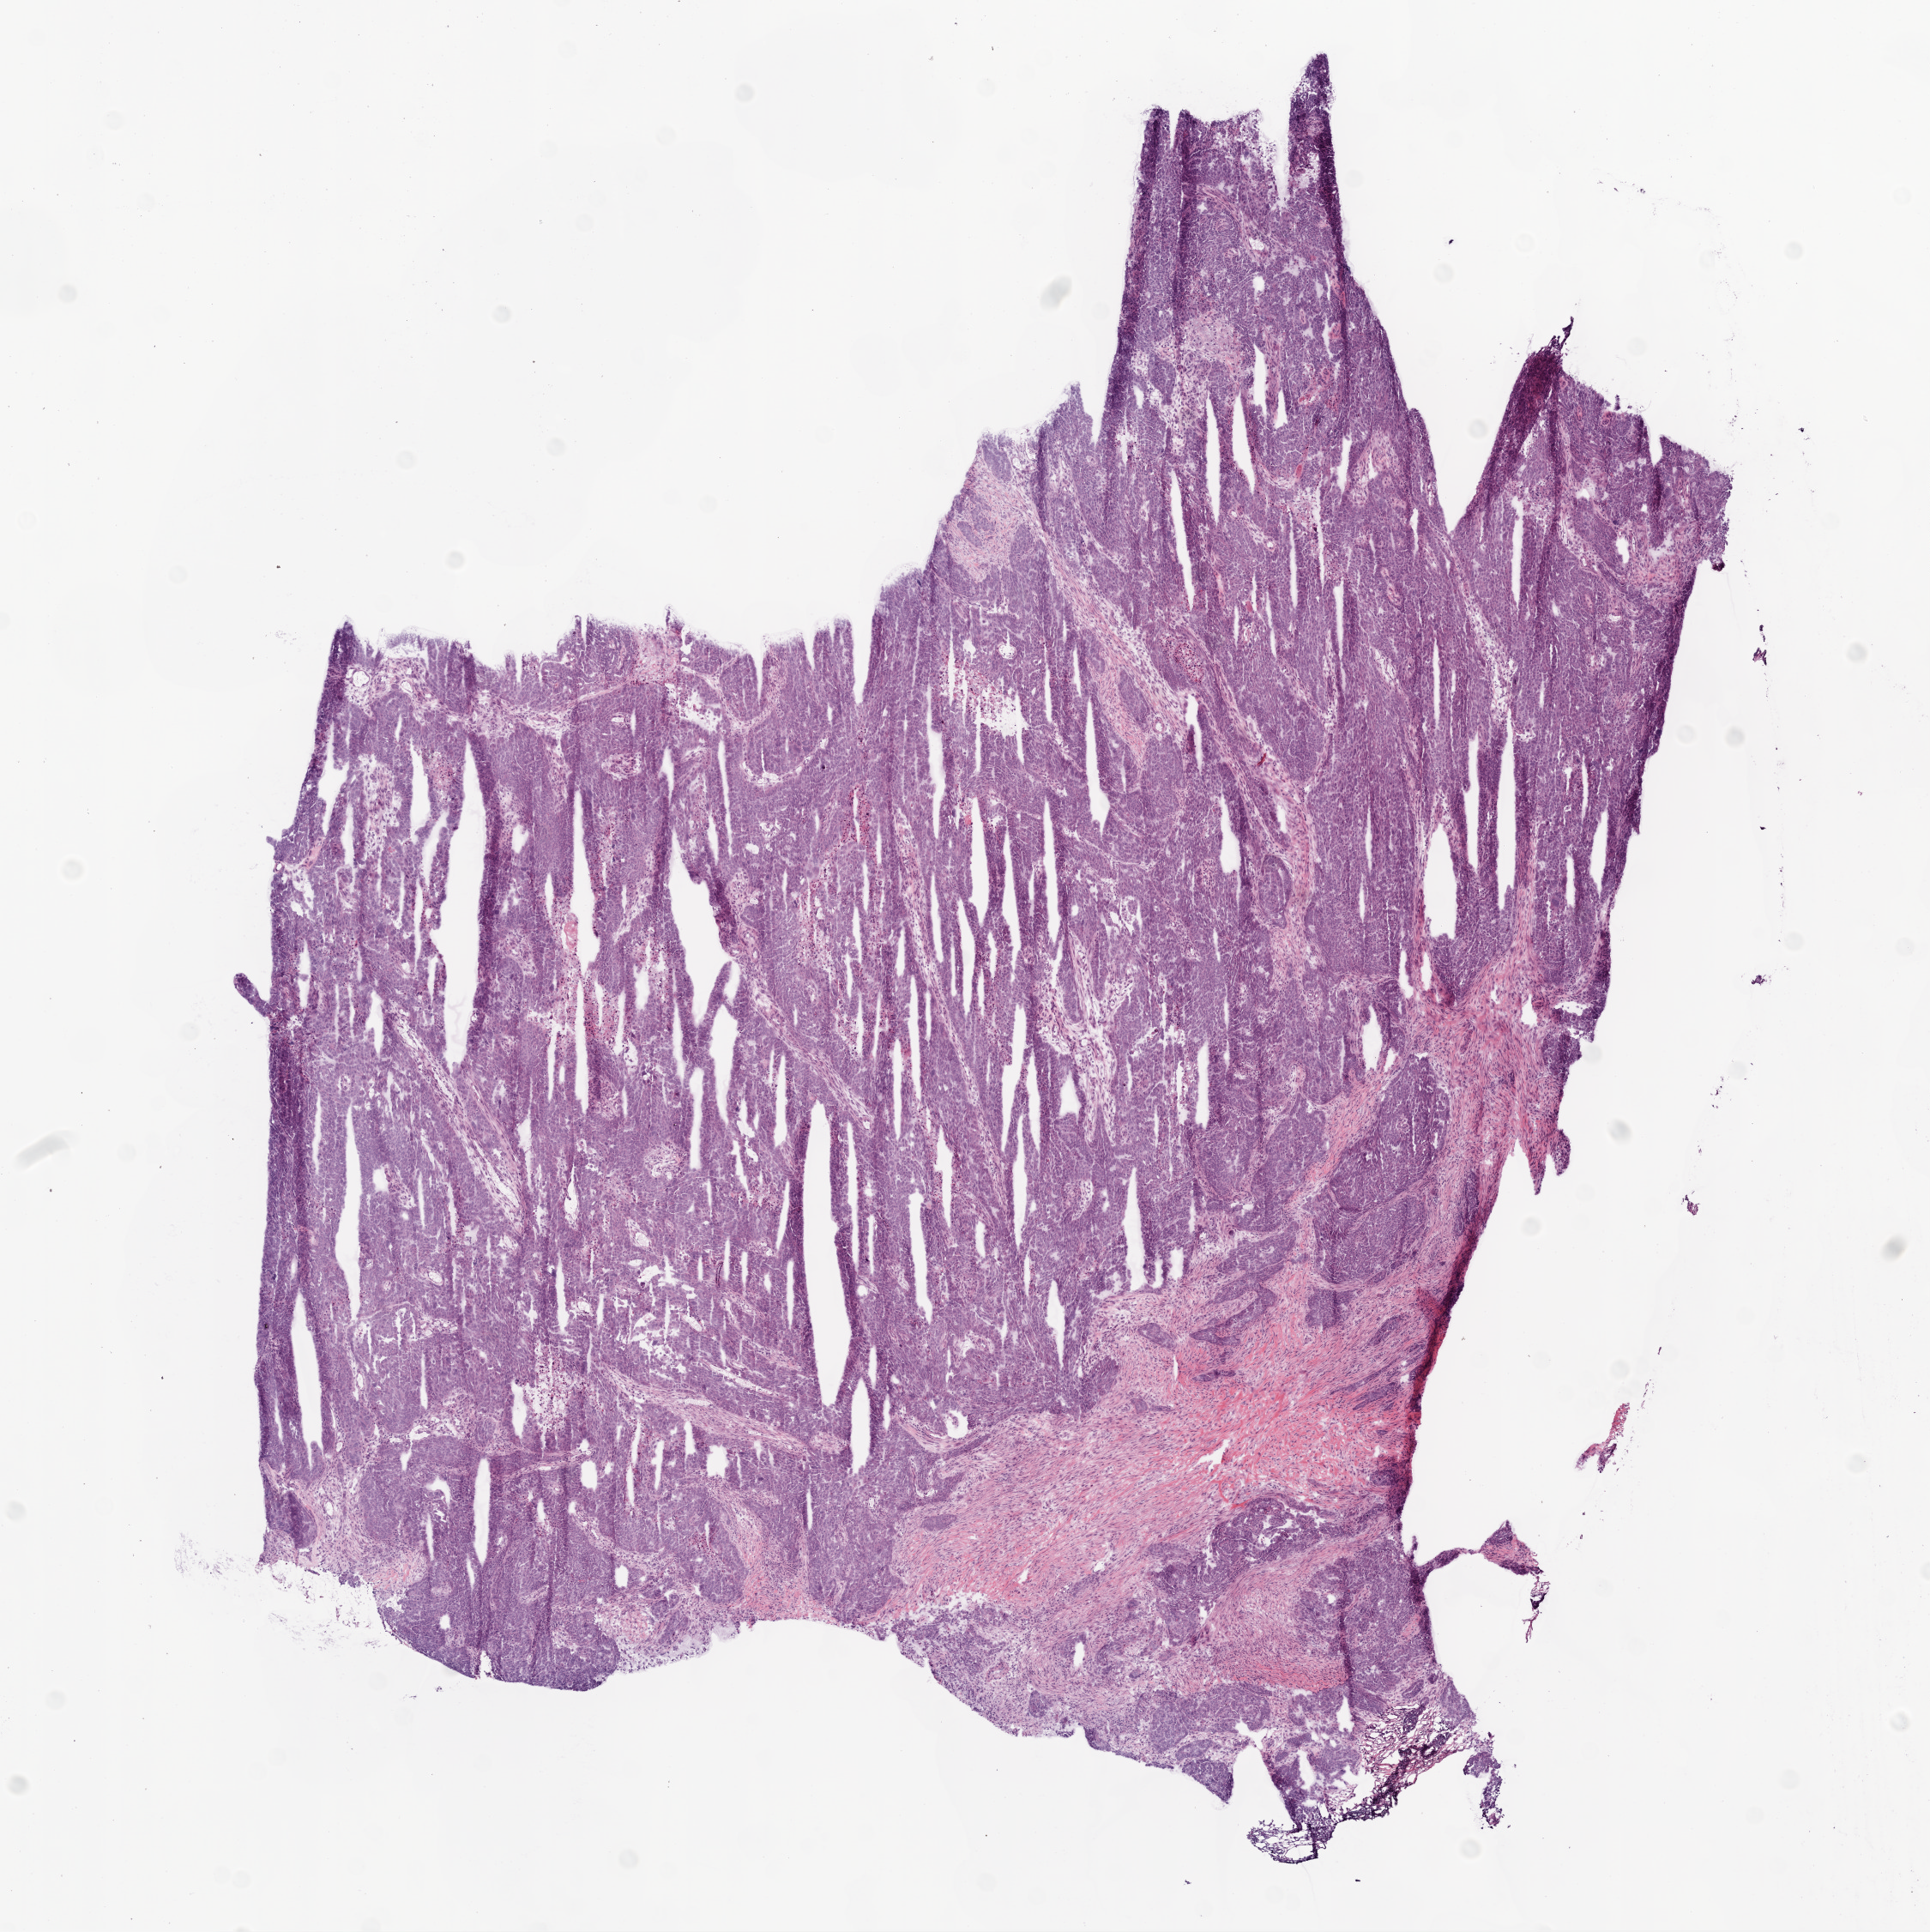
Whole-slide histology image, H&E-stained, a low-resolution overview of the entire scanned area, about 9.0 x 9.0 mm (acquisition: 20x scan). Frozen section. Primary tumour sample from the ovary. Patient: female, age at initial diagnosis 58 years. Histologic grade: G3 (poorly differentiated). Slide review estimates, as recorded: tumour cells 90%, tumour nuclei 90%, normal cells 0%, stromal cells 18%, necrosis 2%.
* laterality: left
* pathologic diagnosis: Serous cystadenocarcinoma, NOS
* FIGO stage: IIIC